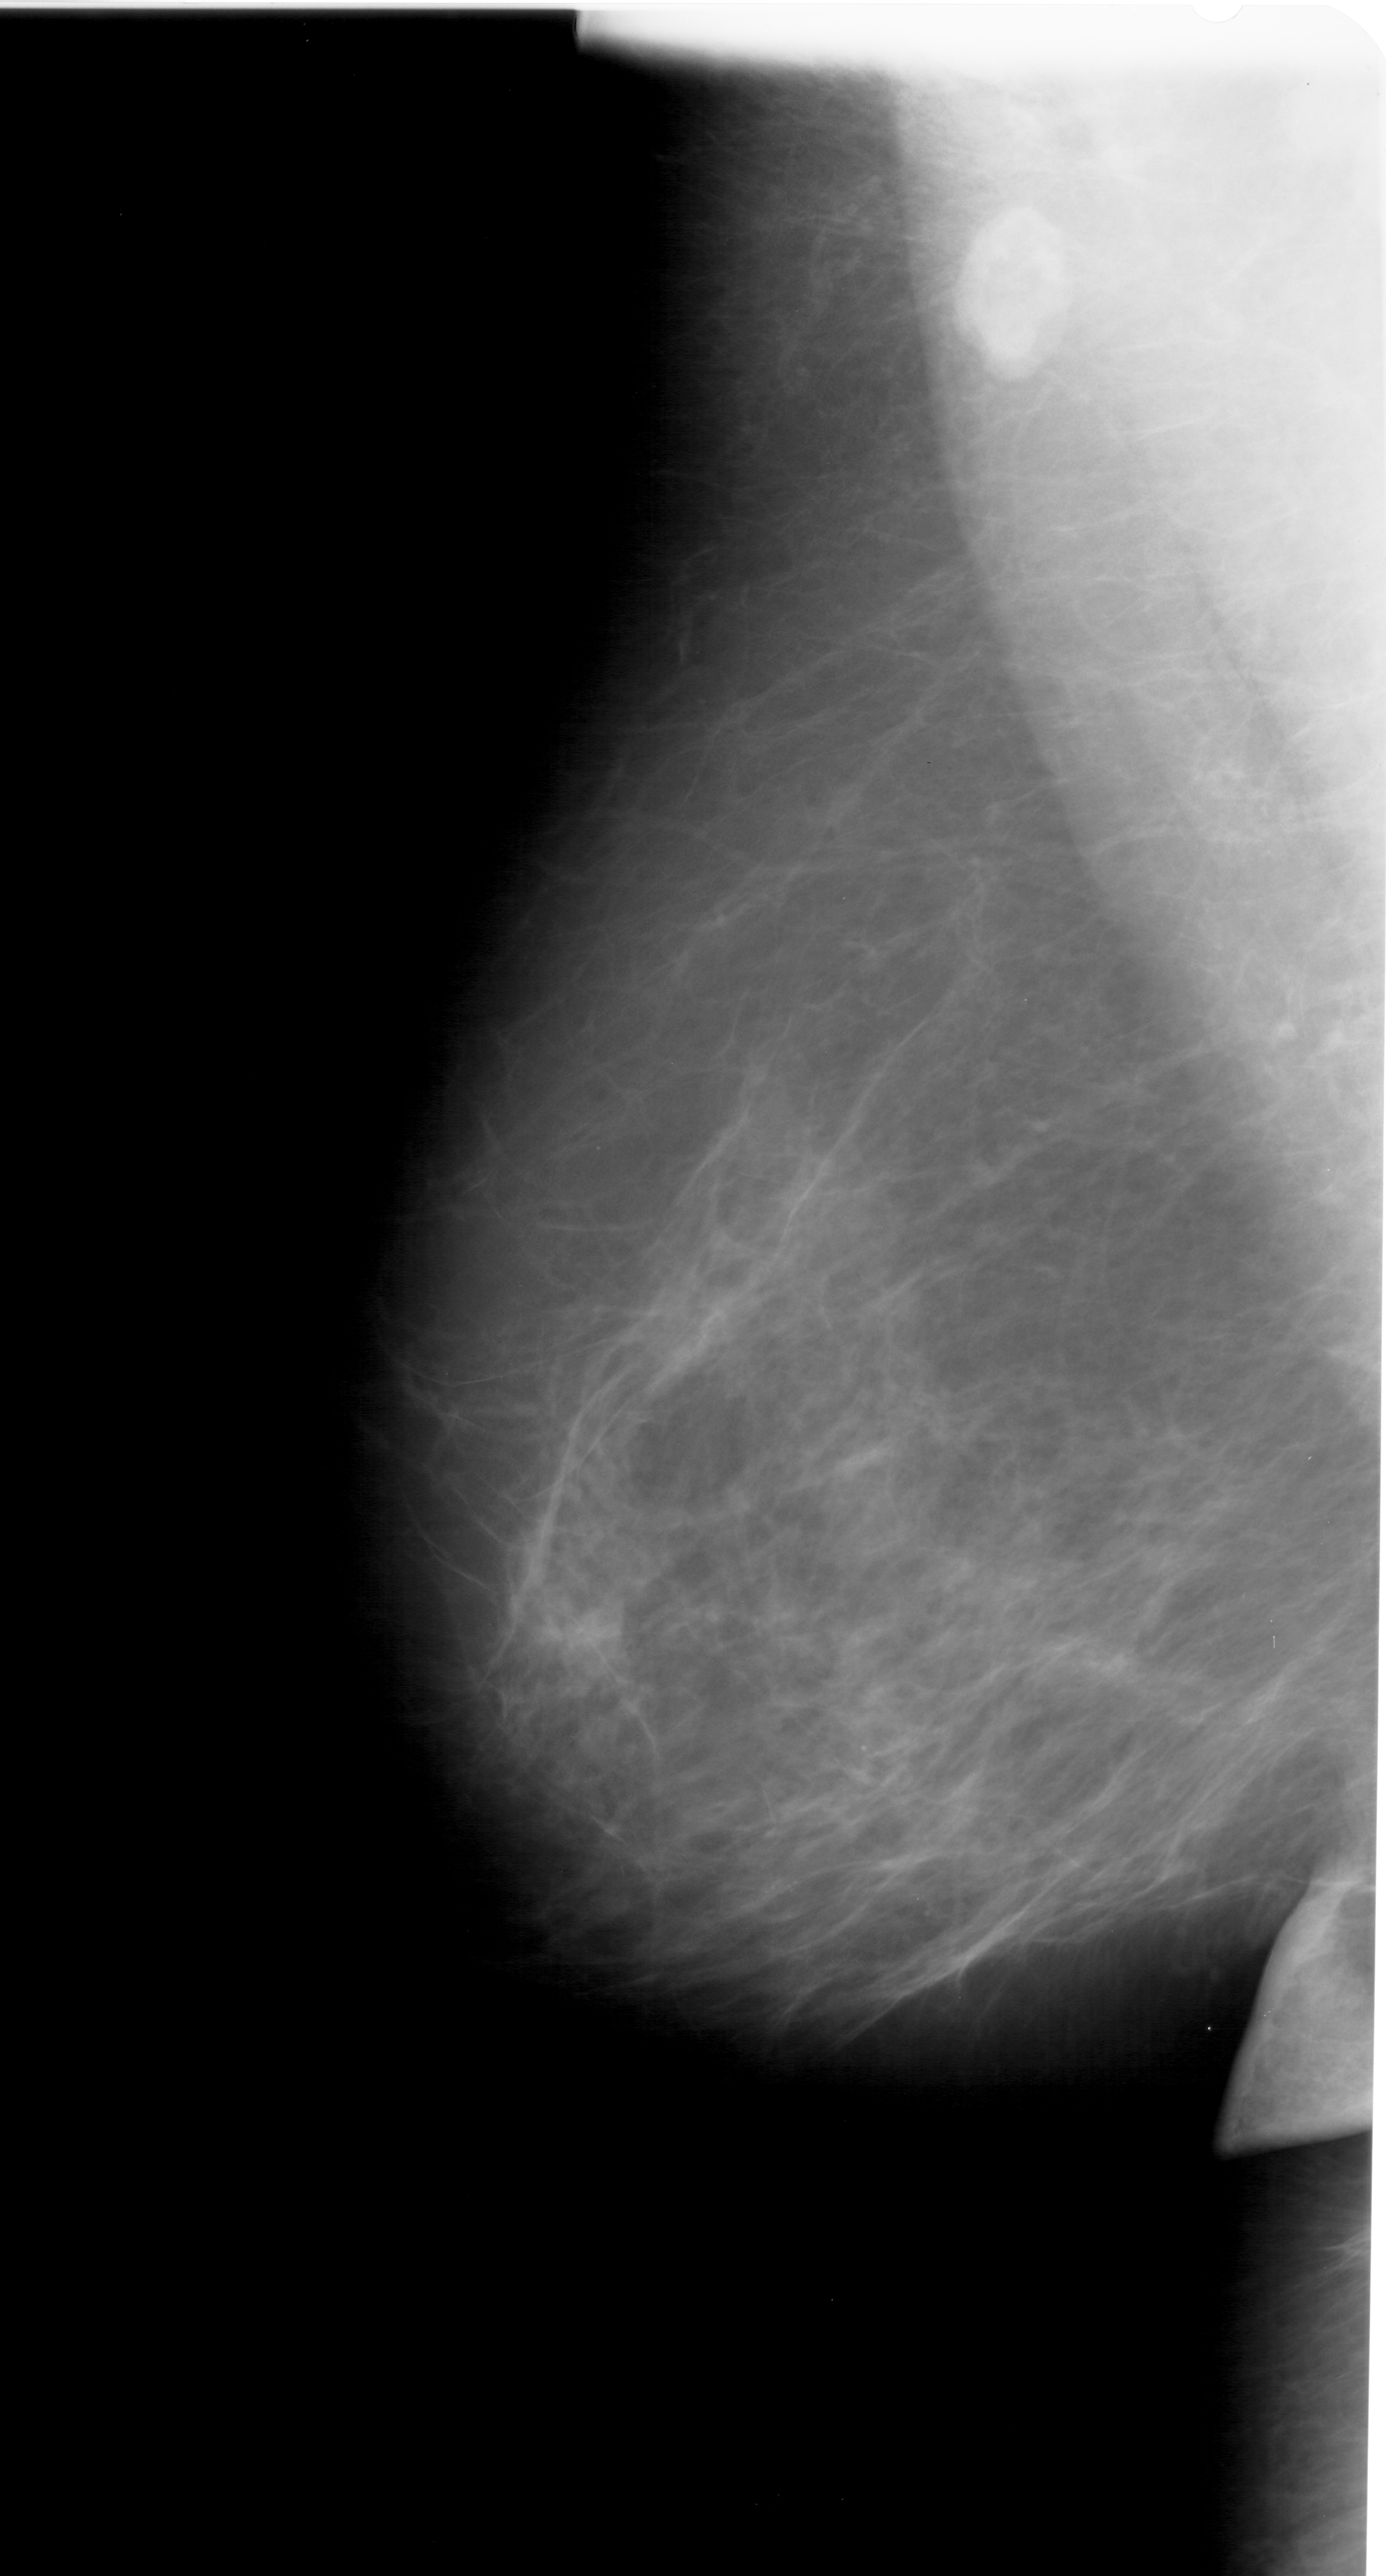
Scanned film-screen mammogram; left breast; MLO view; breast composition: scattered fibroglandular densities (BI-RADS density category 2 of 4); 1386 × 2576 image matrix.
Expert-marked regions of interest on this image (one box per marked abnormality):
- calcifications, morphology pleomorphic, distribution clustered; BI-RADS assessment category 4; subtlety rating 1 on a 1 (subtle) to 5 (obvious) scale; pathology (as recorded): benign: box from (x=742, y=1873) to (x=810, y=1922) px